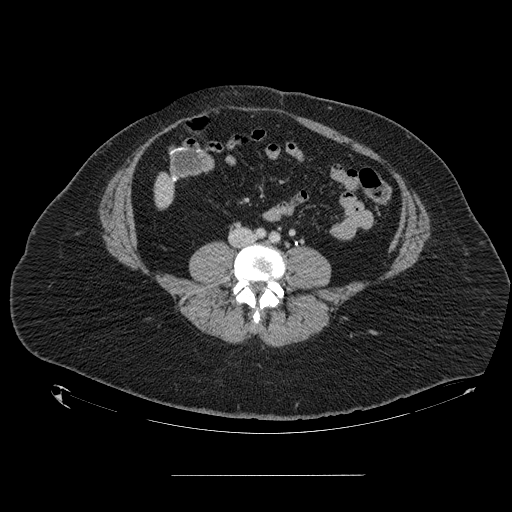
Contrast-enhanced abdominal CT, one axial slice. Slice 10 of 164 in the series (ordered by position). 120 kVp. Intravenous contrast given. Soft-tissue window (W 400 / L 40 HU). 512 × 512 image matrix, field of view 495 × 495 mm. Female patient, age 52 years. Case-level facts recorded for this patient, not image findings: diagnosis: colorectal cancer liver metastases, imaged before liver resection; multiple liver metastases: yes; largest metastasis: 3.5 cm; chemotherapy before resection: no.
Outlined on this slice (manually delineated by an expert):
- liver: box from (x=156, y=175) to (x=175, y=207) px